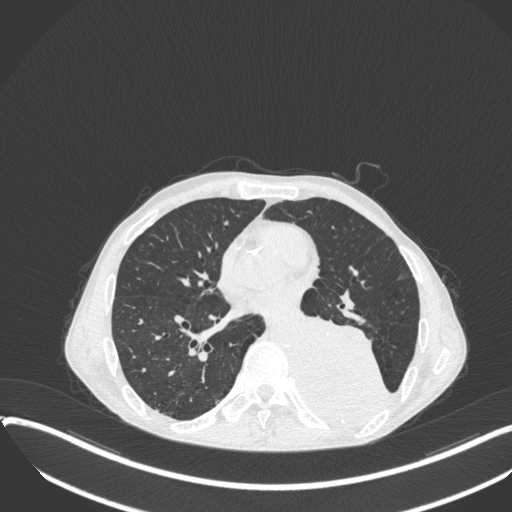
Chest CT, one axial slice; slice 163 of 400 in the series (ordered by position); lung window (W 1500 / L -600 HU); 512 × 512 image matrix, field of view 400 × 400 mm. Patient: male, 57 years. From the clinical record (not read from this slice): clinical TNM (as recorded): T4 N0 M0.
Outlined on this slice (bounding box drawn by a radiologist):
- lung tumour (recorded histology: squamous cell carcinoma): bounding box [x1, y1, x2, y2] px = [297, 309, 391, 425]